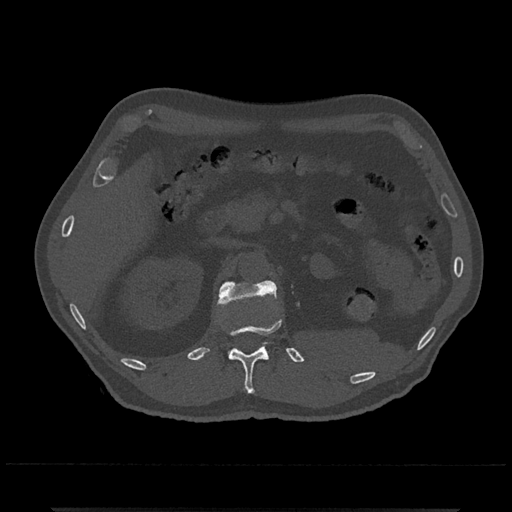
CT including the spine, one axial slice; position 406 of 797 along the scan axis; reconstruction kernel Br40s/3; 120 kVp; bone window (W 1800 / L 400 HU); 0.5 mm slice thickness; 512 × 512 image matrix, field of view 393 × 393 mm. Patient: male, 67 years. From the clinical record (not read from this slice): primary cancer: prostate.
Outlined on this slice (semi-automatic segmentation, software-assisted and operator-edited):
- L1 vertebra: bounding box (x1, y1, x2, y2) in pixels: (218, 280, 277, 359)
- T12 vertebra: (228, 320, 281, 394)